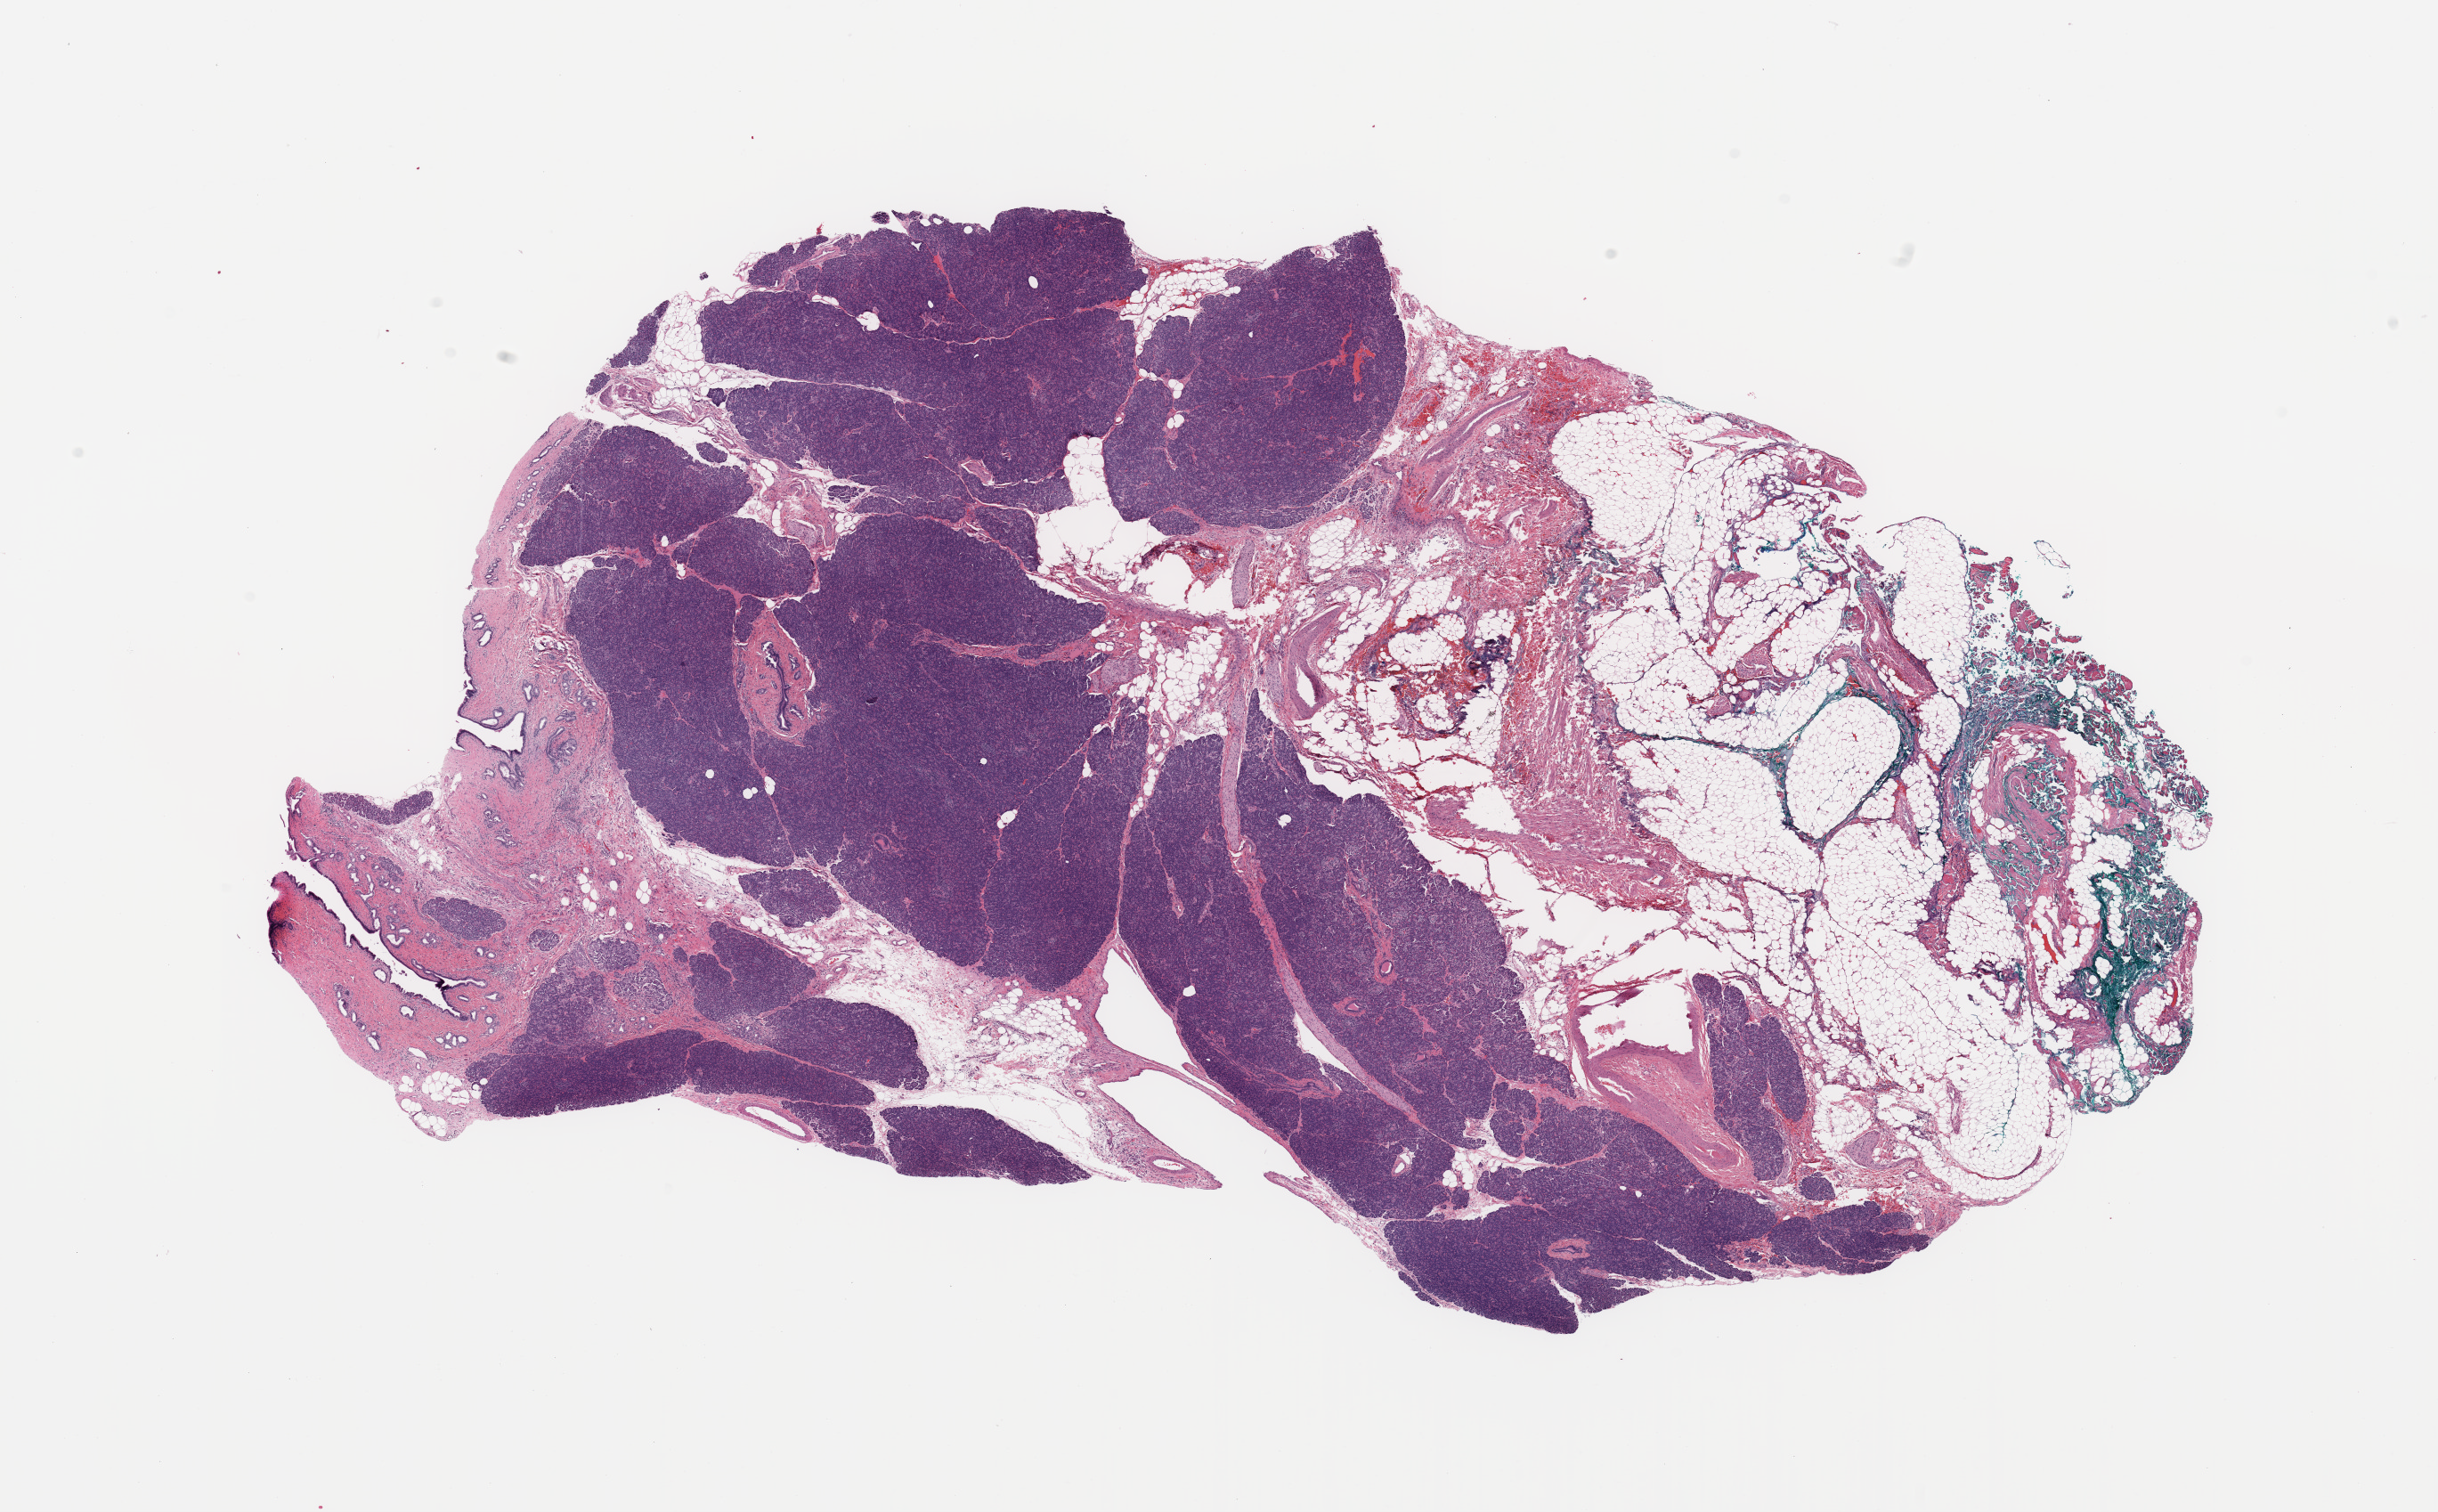
Hematoxylin and eosin (H&E) stained whole-slide image — whole scanned area (about 21.7 x 13.4 mm, from a 20x scan) shown as a low-resolution overview; normal (non-tumour) tissue sample, sampled site: pancreas. Female, 38 y/o.
* this section: normal (non-tumour) tissue from the same patient
* patient diagnosis: Infiltrating duct carcinoma, NOS